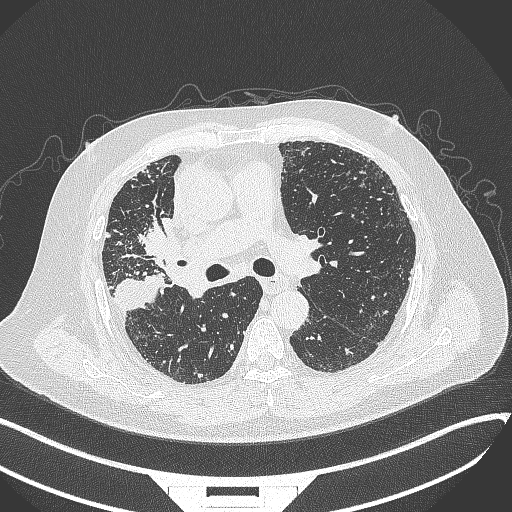
Chest CT, one axial slice. Position 206 of 384 along the scan axis. Reconstruction kernel B70f. 120 kVp. Lung window (W 1500 / L -600 HU). 1 mm slice thickness. 512 × 512 image matrix, field of view 400 × 400 mm. Male patient, age 69 years. Case-level facts recorded for this patient, not image findings: clinical TNM (as recorded): T4 N3 M1.
Annotated regions visible in this slice (bounding box drawn by a radiologist):
- lung tumour (recorded histology: adenocarcinoma): bounding box [x1, y1, x2, y2] px = [132, 211, 183, 263]